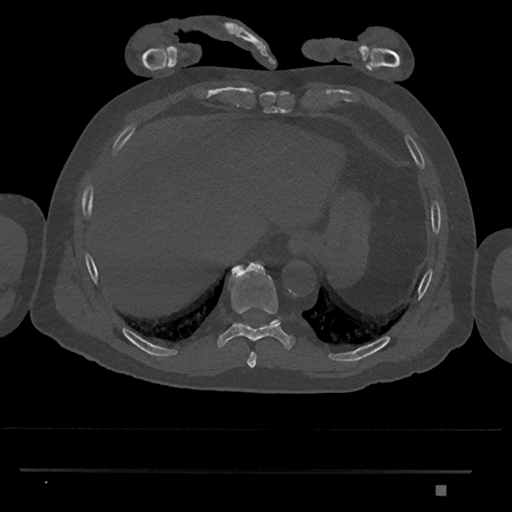
CT including the spine, one axial slice. Position 1052 of 1134 along the scan axis. Bone window (W 1800 / L 400 HU). 0.5 mm slice thickness. 512 × 512 image matrix, field of view 429 × 429 mm. Patient: male, 65 years. Case-level facts recorded for this patient, not image findings: primary cancer: prostate.
Structures marked on this image (semi-automatically segmented with operator editing):
- T10 vertebra: bounding box [x1, y1, x2, y2] px = [272, 319, 281, 324]
- T8 vertebra: [246, 352, 257, 367]
- T9 vertebra: [217, 262, 296, 349]